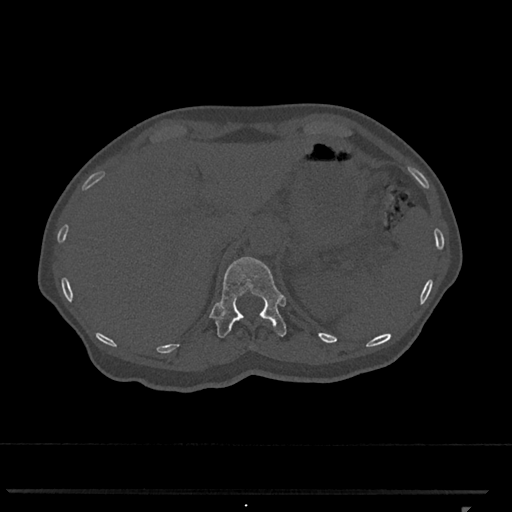
CT including the spine, one axial slice. Position 474 of 793 along the scan axis. Reconstruction kernel Br40s/3. 120 kVp. Bone window (W 1800 / L 400 HU). 512 × 512 image matrix, field of view 380 × 380 mm. Female patient, age 62 years. Case-level facts recorded for this patient, not image findings: primary cancer: renal.
Outlined on this slice (semi-automatic segmentation, software-assisted and operator-edited):
- T12 vertebra: bounding box (x1, y1, x2, y2) in pixels: (216, 257, 286, 338)